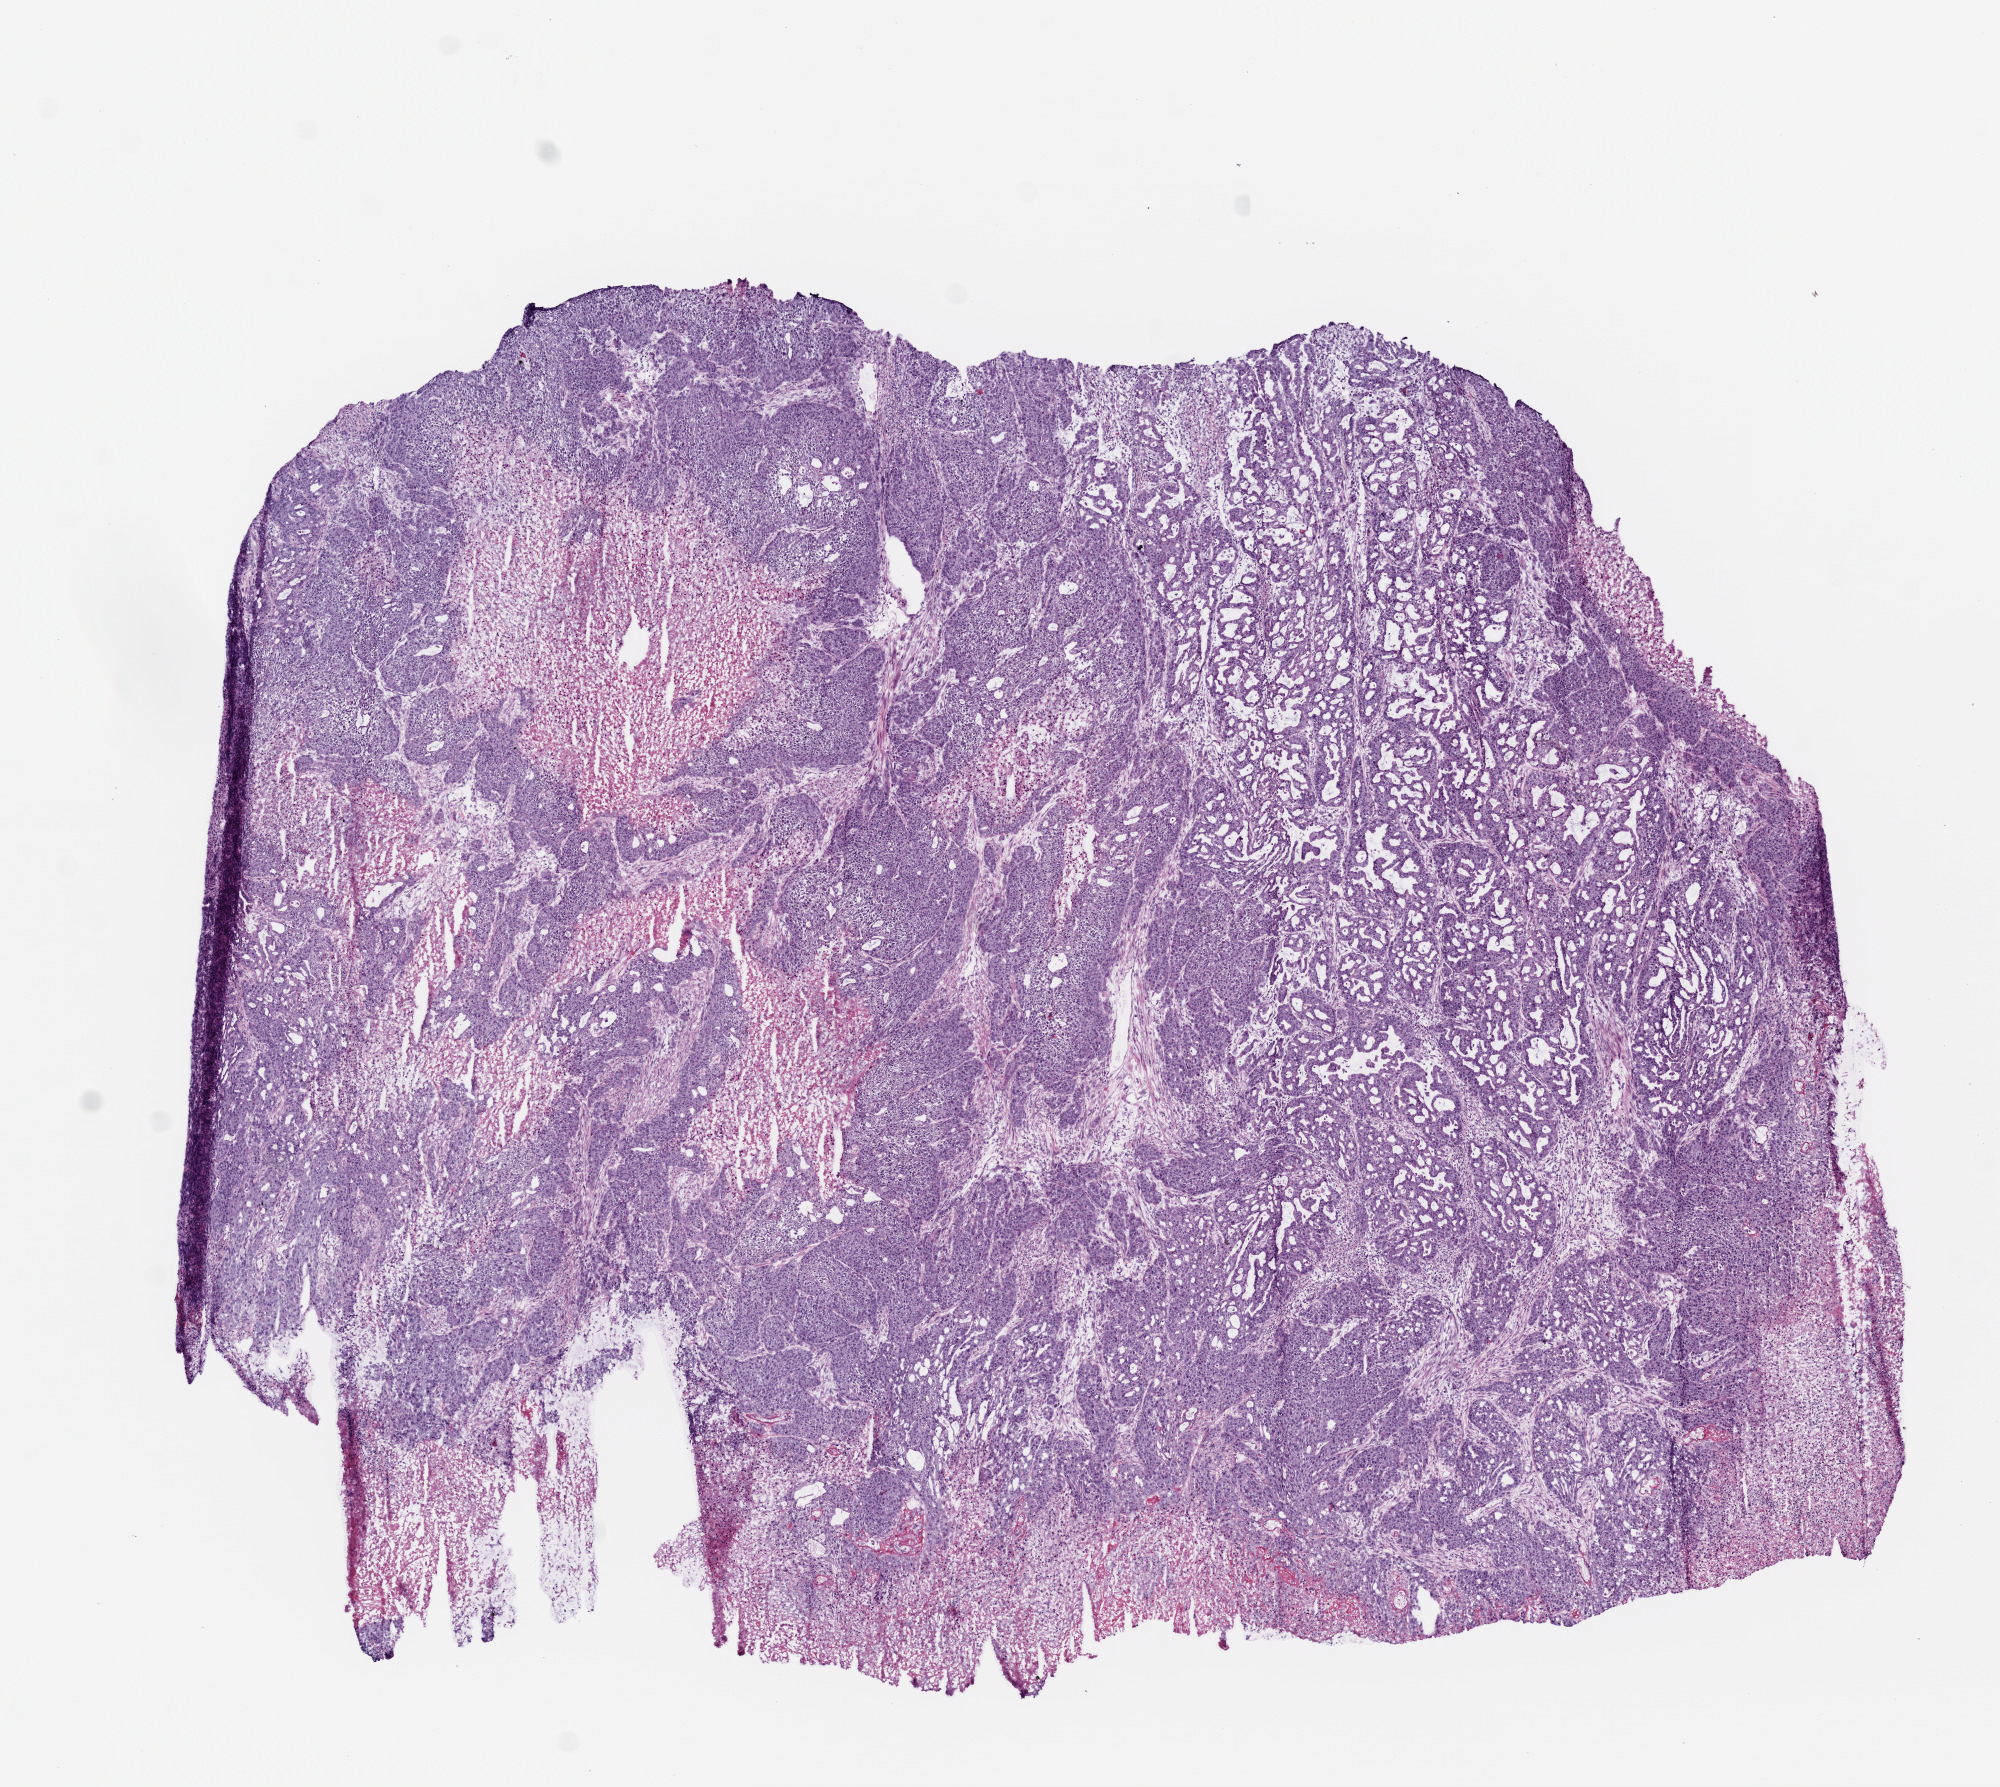
Whole-slide histology image, H&E-stained, low-resolution overview of the scanned area, about 8.0 x 7.2 mm; frozen section from the bottom of the tissue portion; primary tumour sample from the stomach. Patient: male, age at initial diagnosis 85 years. Histologic grade: G3 (poorly differentiated). Slide review estimates, as recorded: tumour cells 75%, tumour nuclei 75%, normal cells 0%, stromal cells 10%, necrosis 15%.
• AJCC pathologic stage: IB (5th edition)
• histologic diagnosis: Adenocarcinoma, intestinal type (gastric antrum)
• TNM: T2 N0 M0